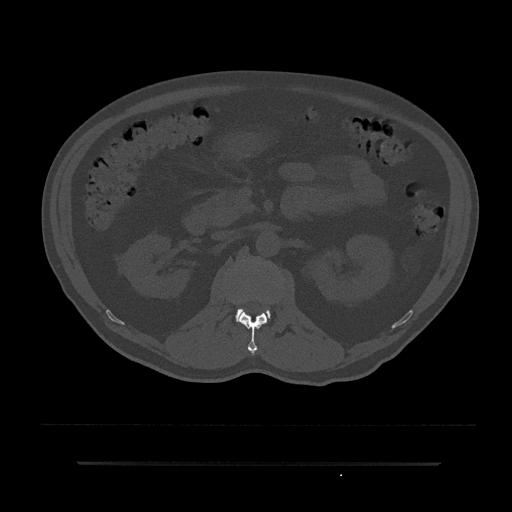
CT including the spine, one axial slice; slice 114 of 797 in the series (ordered by position); reconstruction kernel Br40s/3; bone window (W 1800 / L 400 HU); 512 × 512 image matrix. Patient: male, 59 years. From the clinical record (not read from this slice): primary cancer: bile ducts.
Outlined on this slice (semi-automatically segmented with operator editing):
- L1 vertebra: box from (x=238, y=312) to (x=268, y=355) px
- L2 vertebra: (x=236, y=308)–(x=270, y=321)